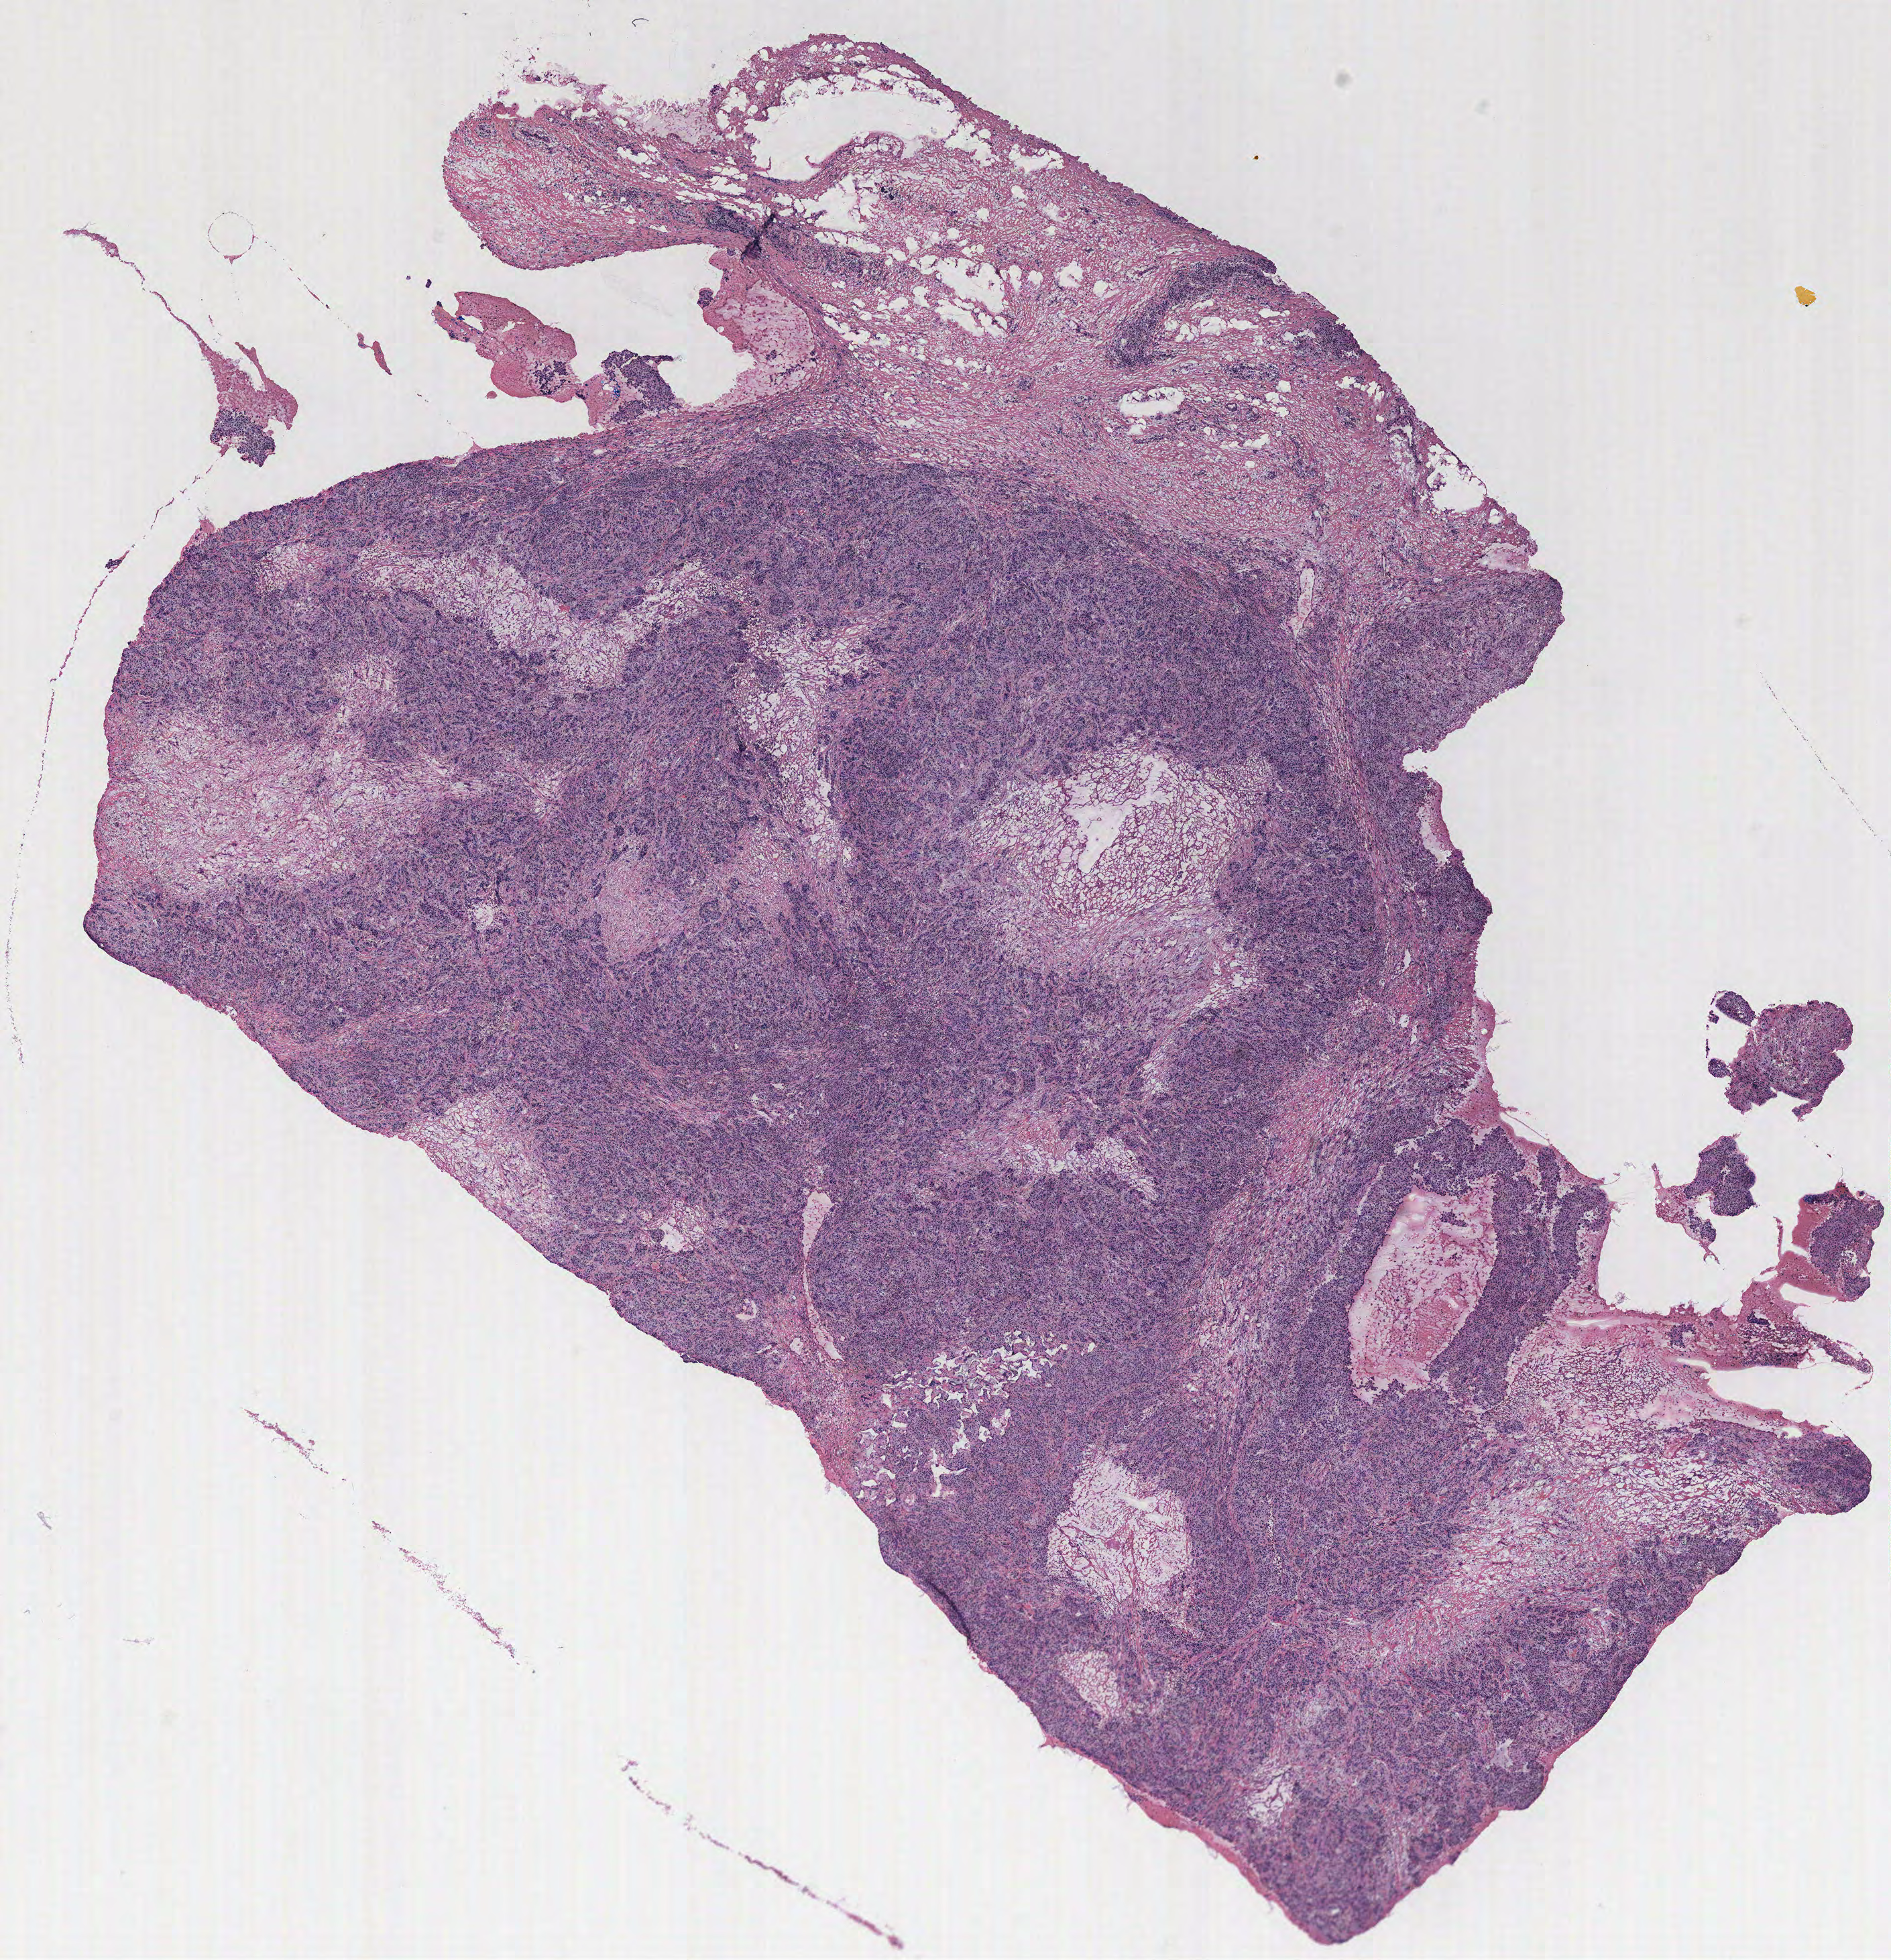
H&E-stained whole-slide image — a low-resolution overview of the entire scanned area, about 11.3 x 11.7 mm; tumour tissue sample, breast. Female, 55 y/o.
* AJCC pathologic stage: IIA
* histologic diagnosis: Infiltrating duct carcinoma, NOS